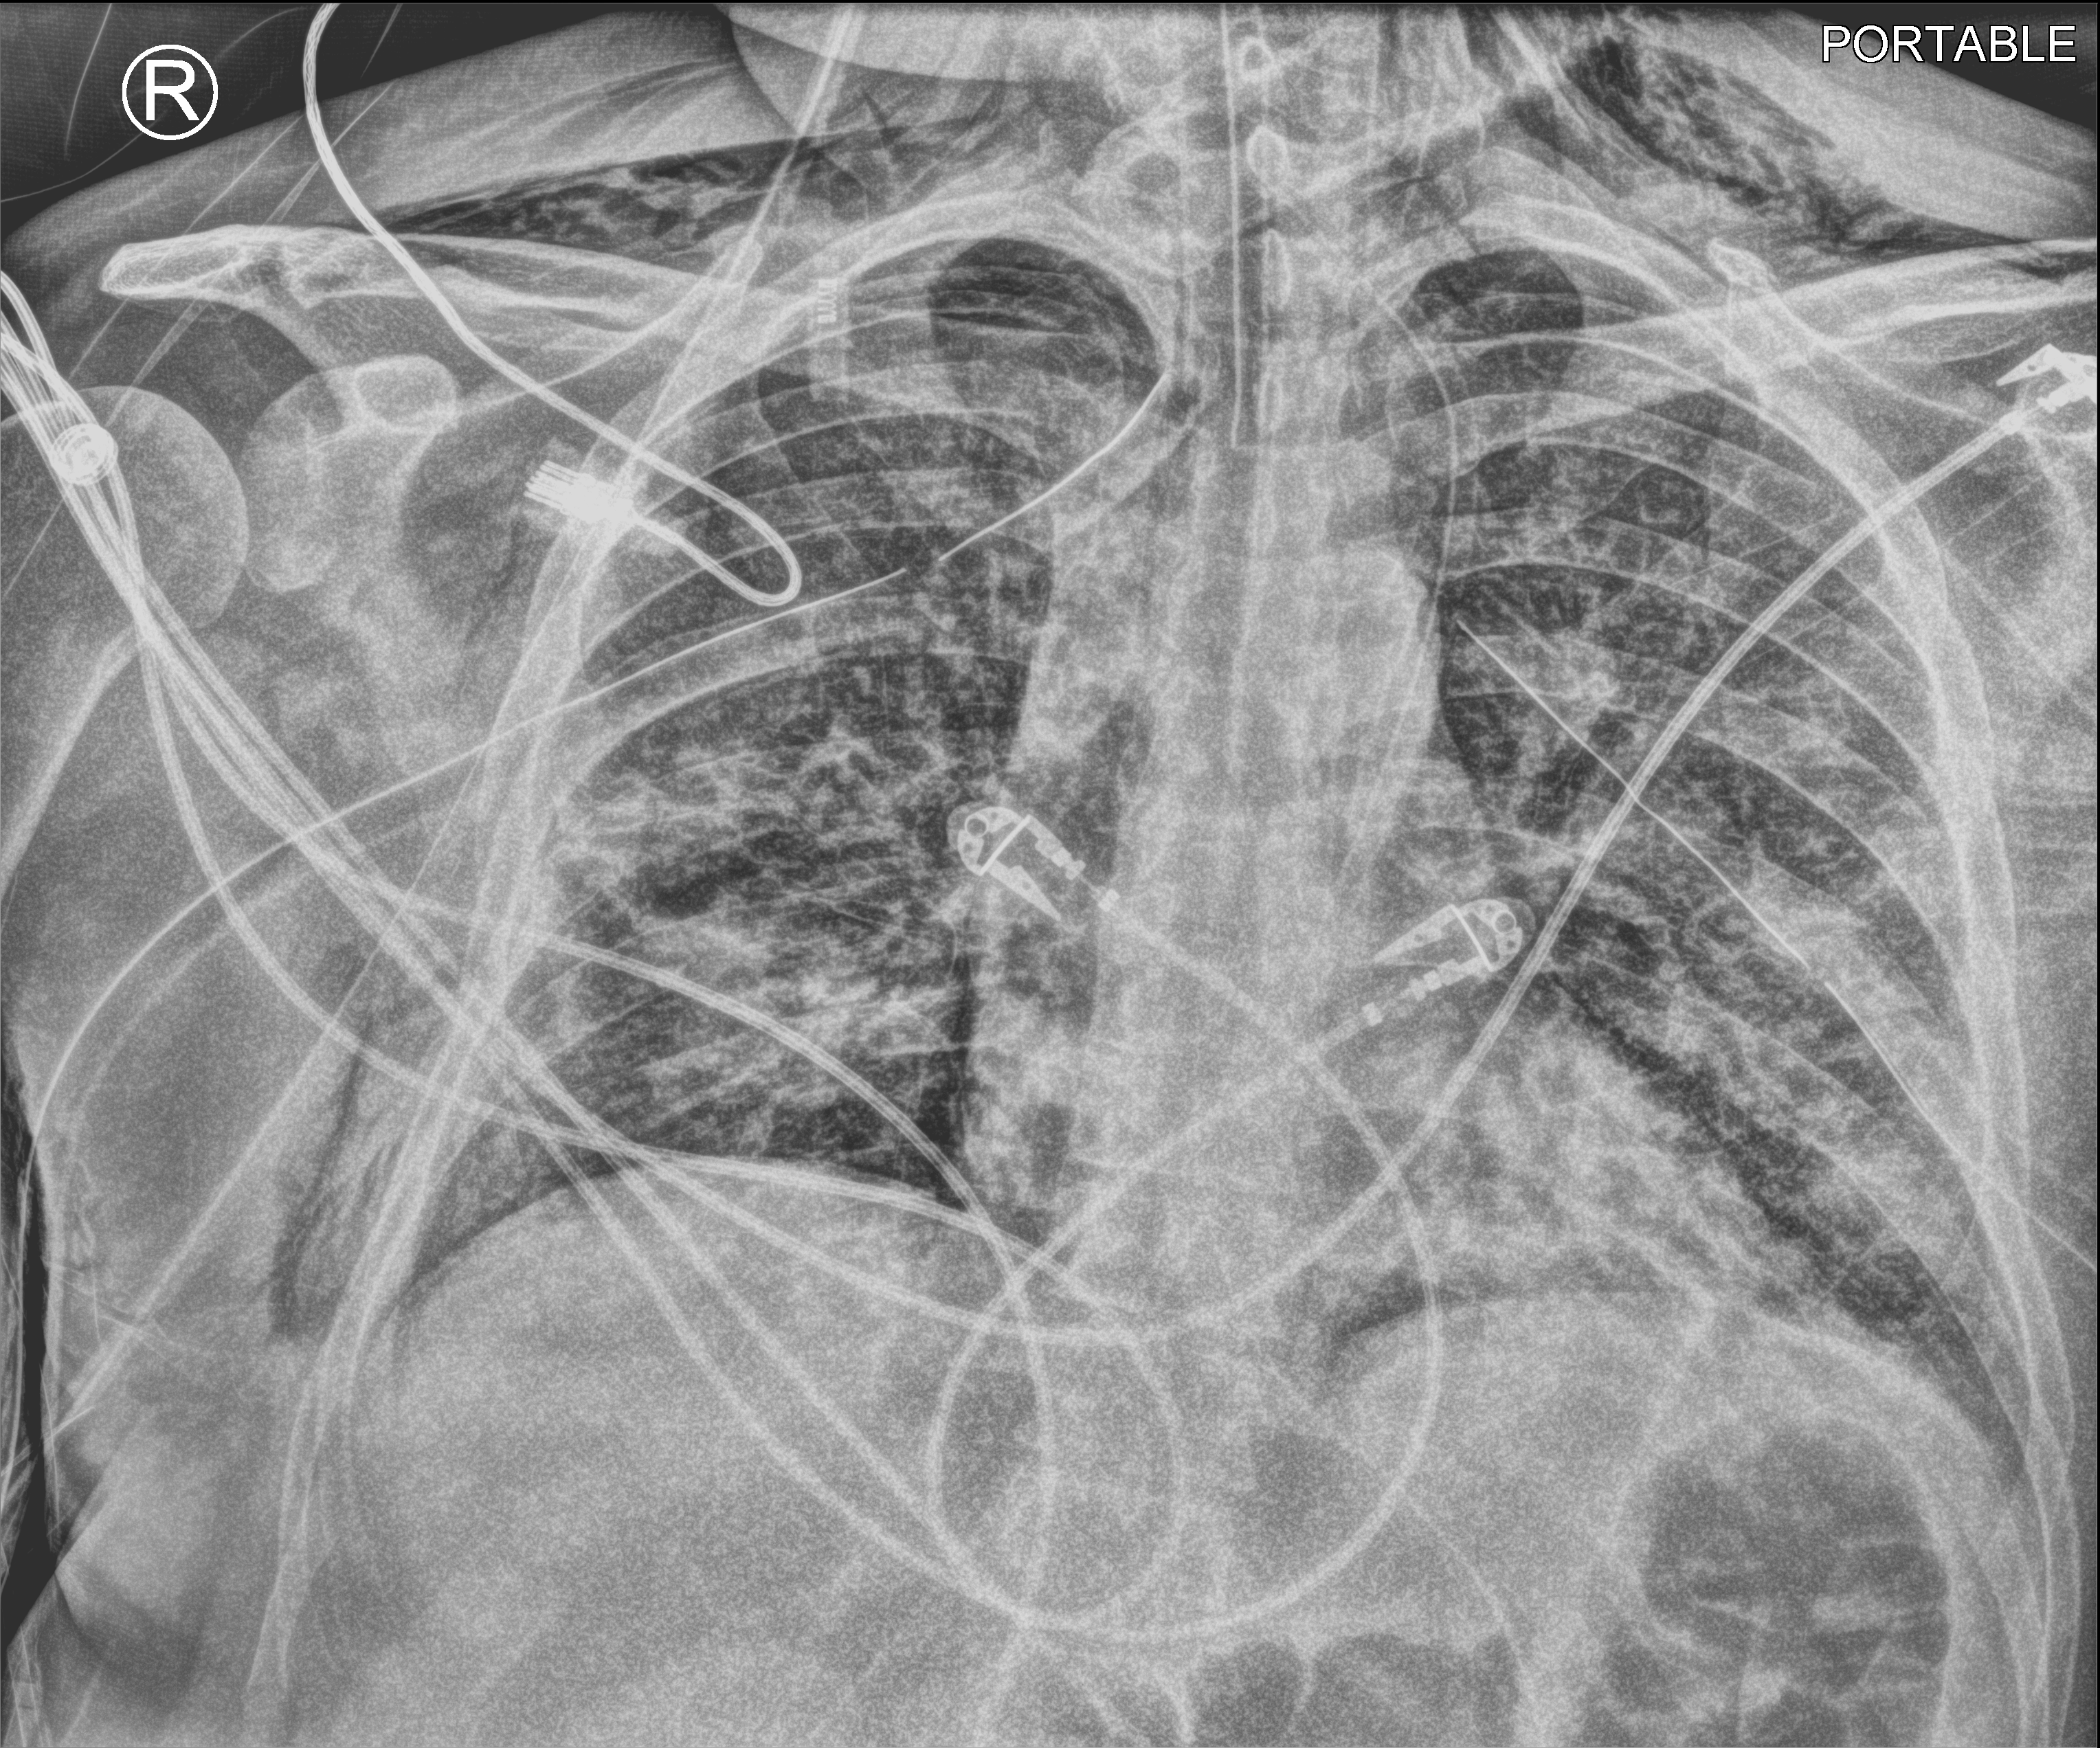
Chest X-ray (portable); anteroposterior (AP) projection. Male patient hospitalised with COVID-19, age 18–59 years.
Hospital-stay facts (about this admission, not read from this image; timing relative to this image not recorded): mechanically ventilated during this hospital stay: yes.